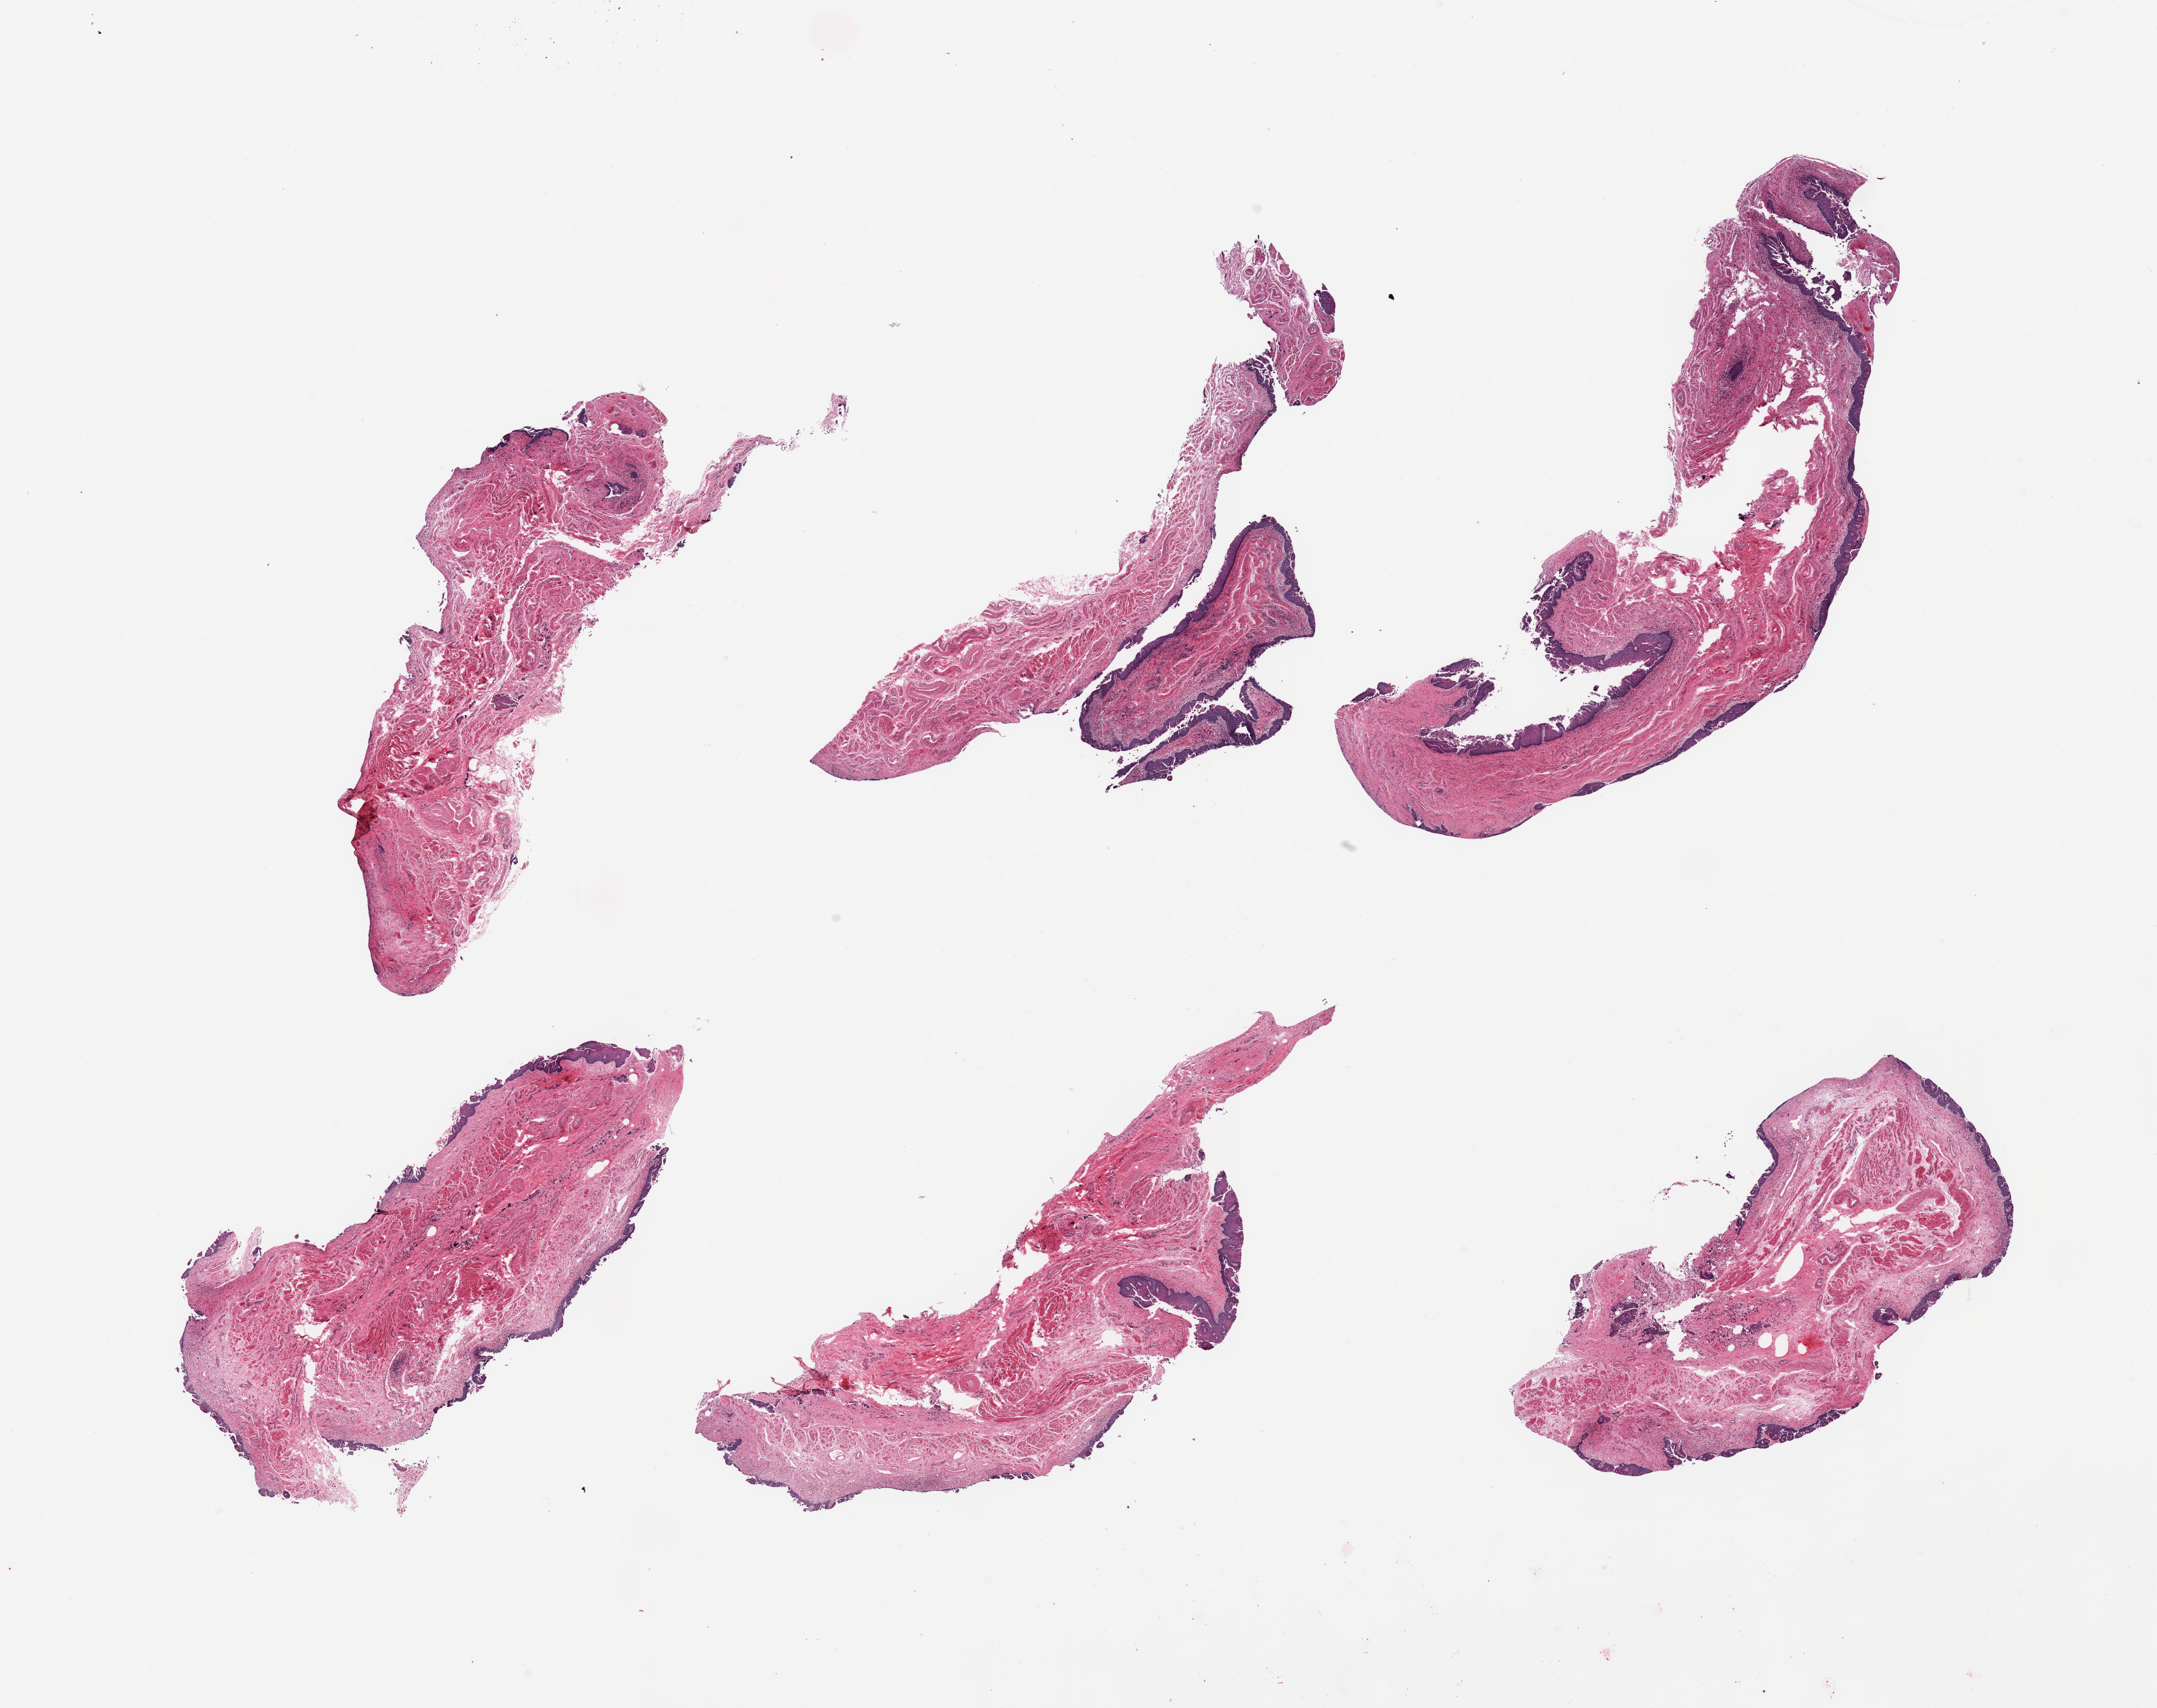
H&E whole-slide image, brightfield — a low-resolution overview of the entire scanned area, about 25.6 x 20.3 mm, PAXgene-fixed paraffin-embedded (PFPE) section, sampled site (target tissue): esophageal mucous membrane, donor tissue sample. Donor sex: female.
Review note (as recorded): 6 pieces, partial sloughing of squamous mucosa, residual up to ~0.25mm.